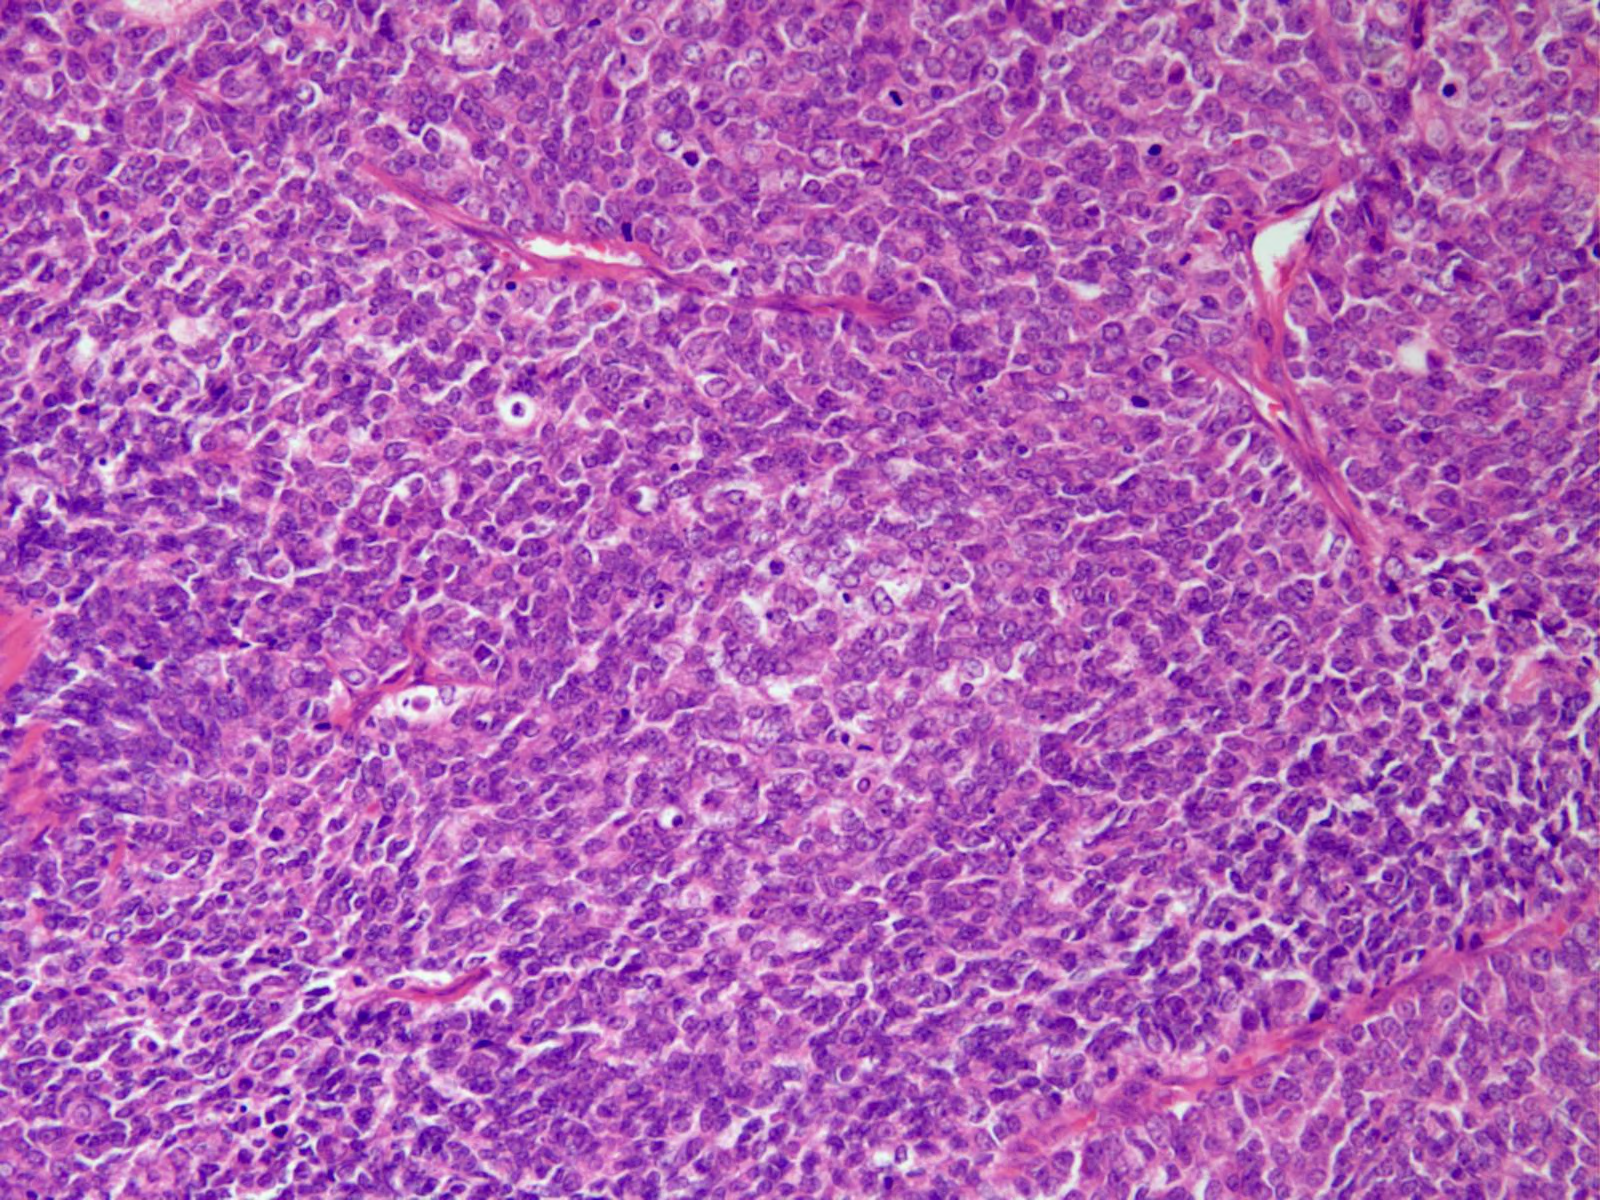
Hematoxylin and eosin (H&E) stained micrograph of a single small tissue field, roughly 0.8 x 0.6 mm in extent. Formalin-fixed paraffin-embedded (FFPE) diagnostic section. Sample: primary tumour, stomach. Female, age 60 years at initial diagnosis. Histologic grade: G3 (poorly differentiated).
Histologic diagnosis: Adenocarcinoma, NOS (body of stomach).